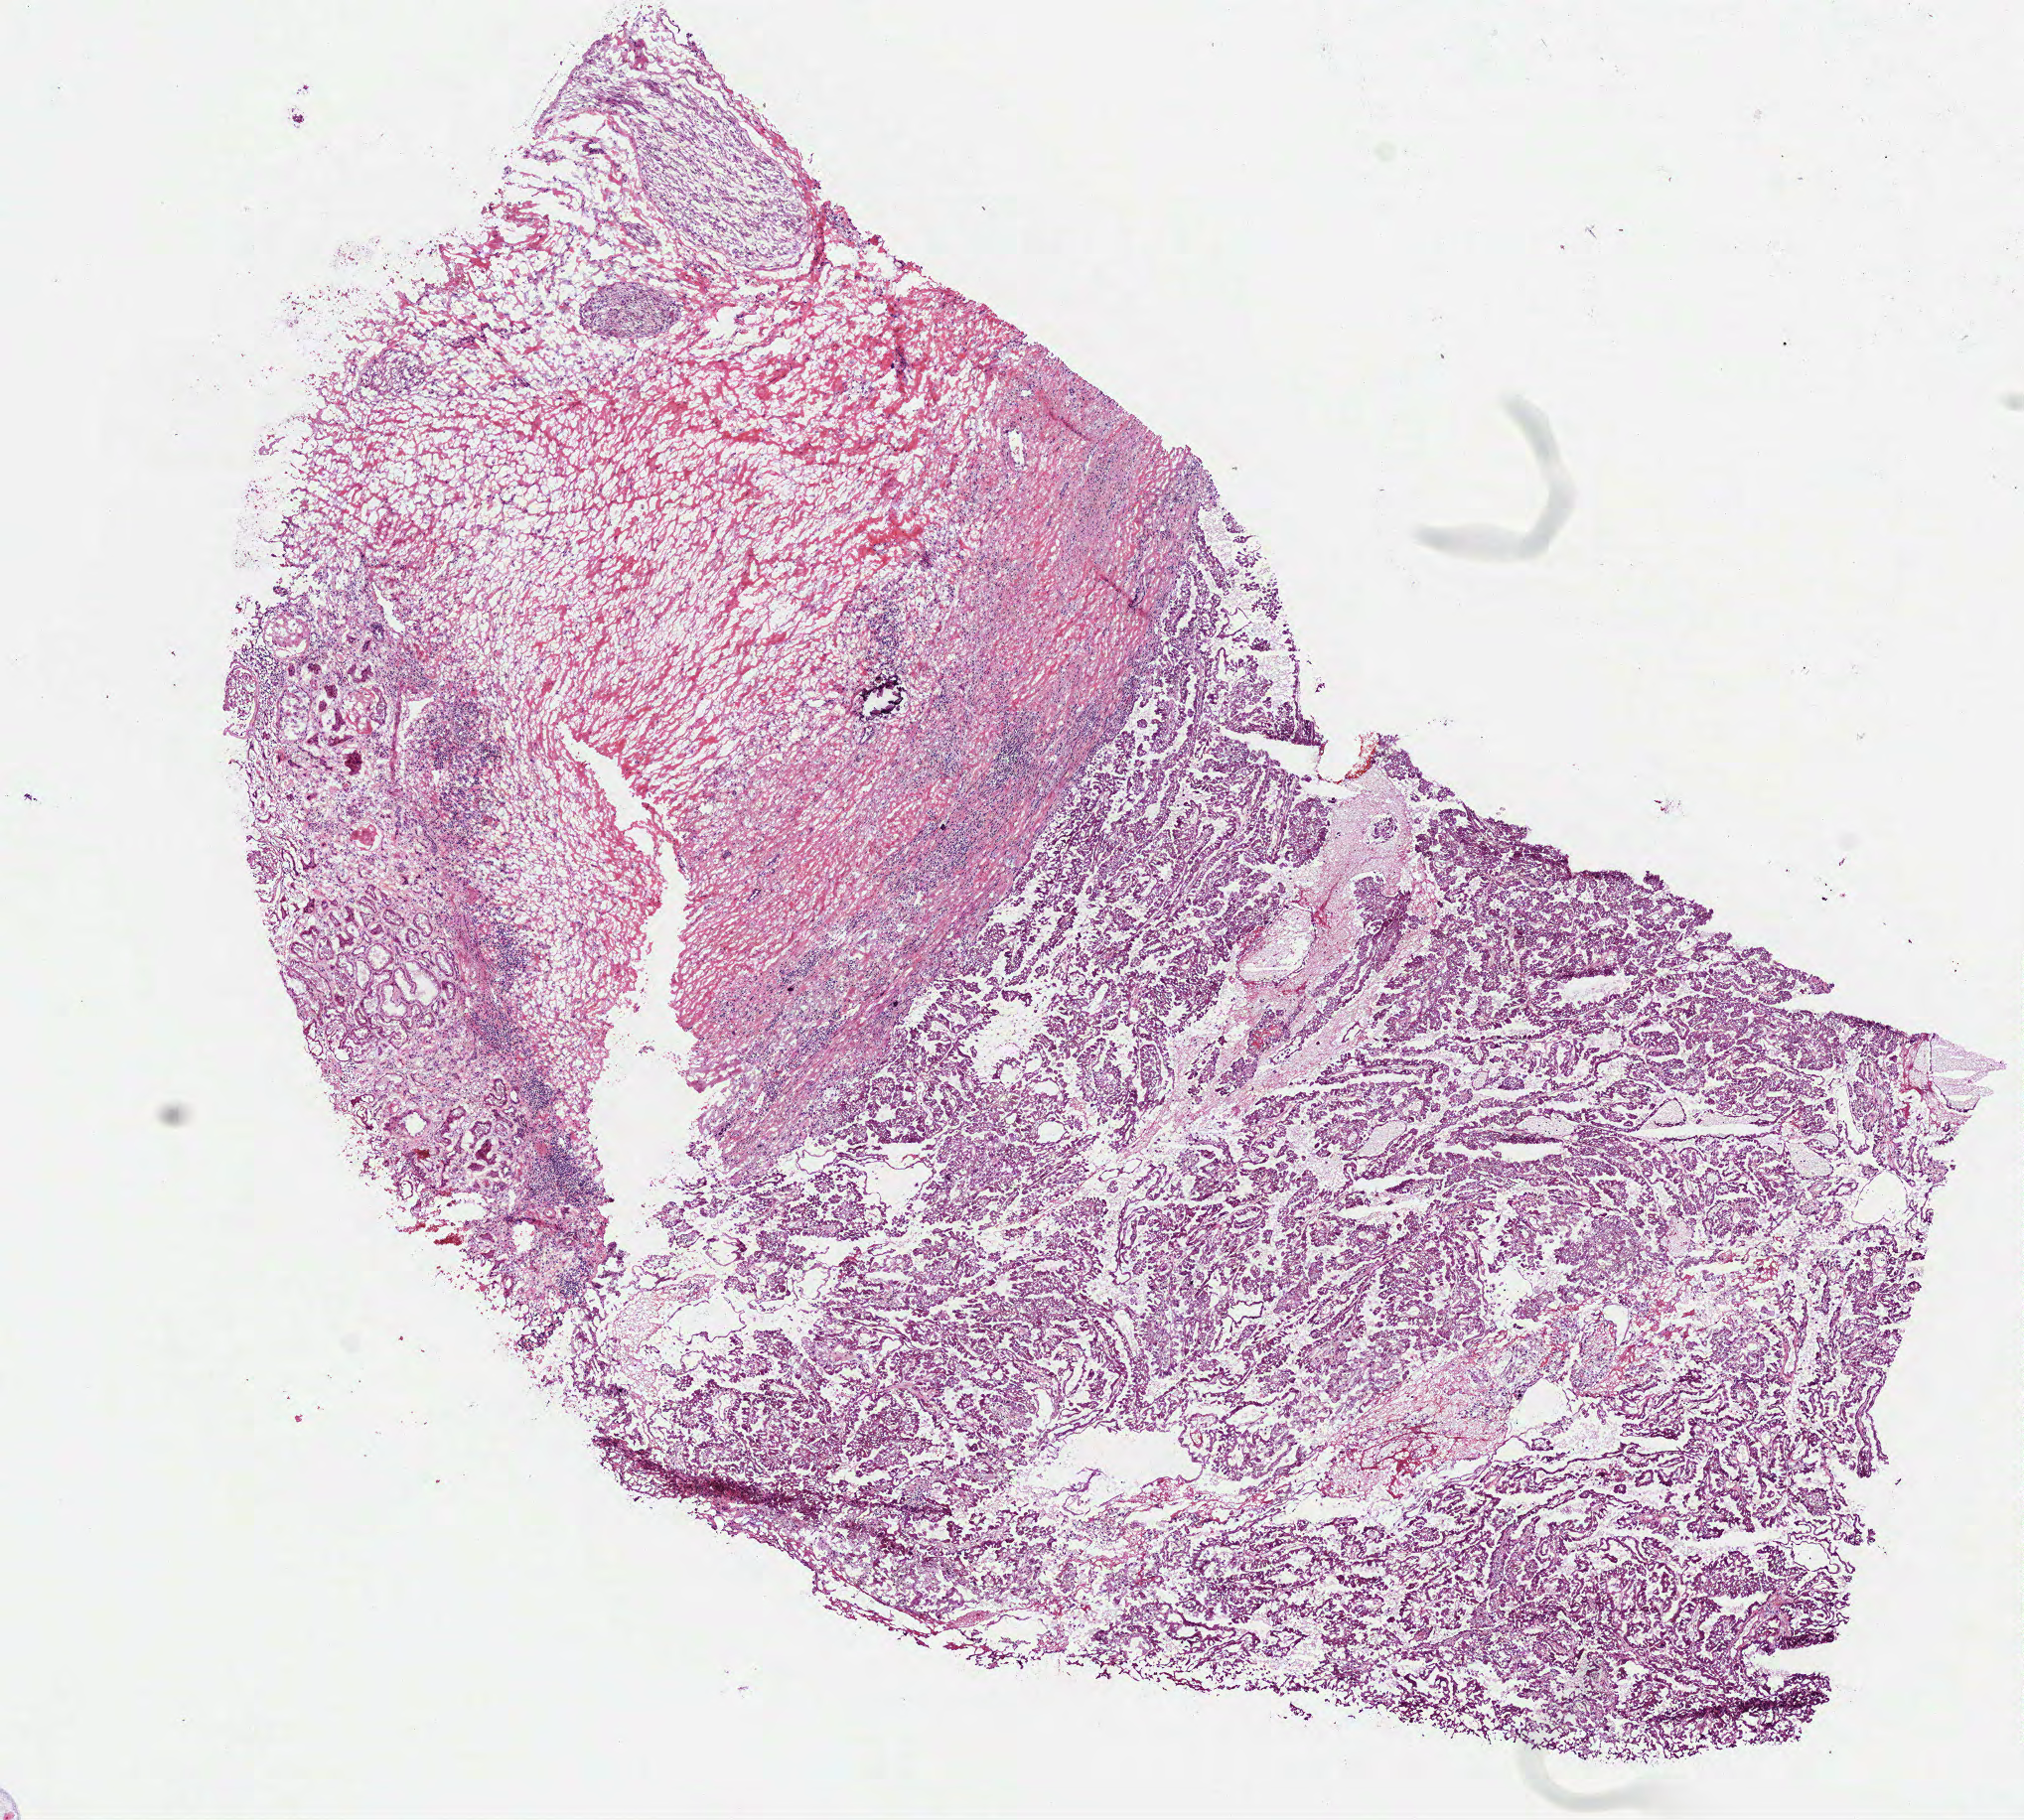
Hematoxylin and eosin (H&E) stained whole-slide image, low-resolution overview of the scanned area, about 8.2 x 7.4 mm (acquisition: 40x scan), frozen section from the bottom of the tissue portion, kidney, primary tumour sample. Patient: male, age at initial diagnosis 67 years. Composition of this section per pathologist review: tumour cells 50%, tumour nuclei 75%, normal cells 8%, stromal cells 42%, necrosis 0%.
Histologic diagnosis: Papillary adenocarcinoma, NOS. AJCC pathologic stage: III (6th edition).